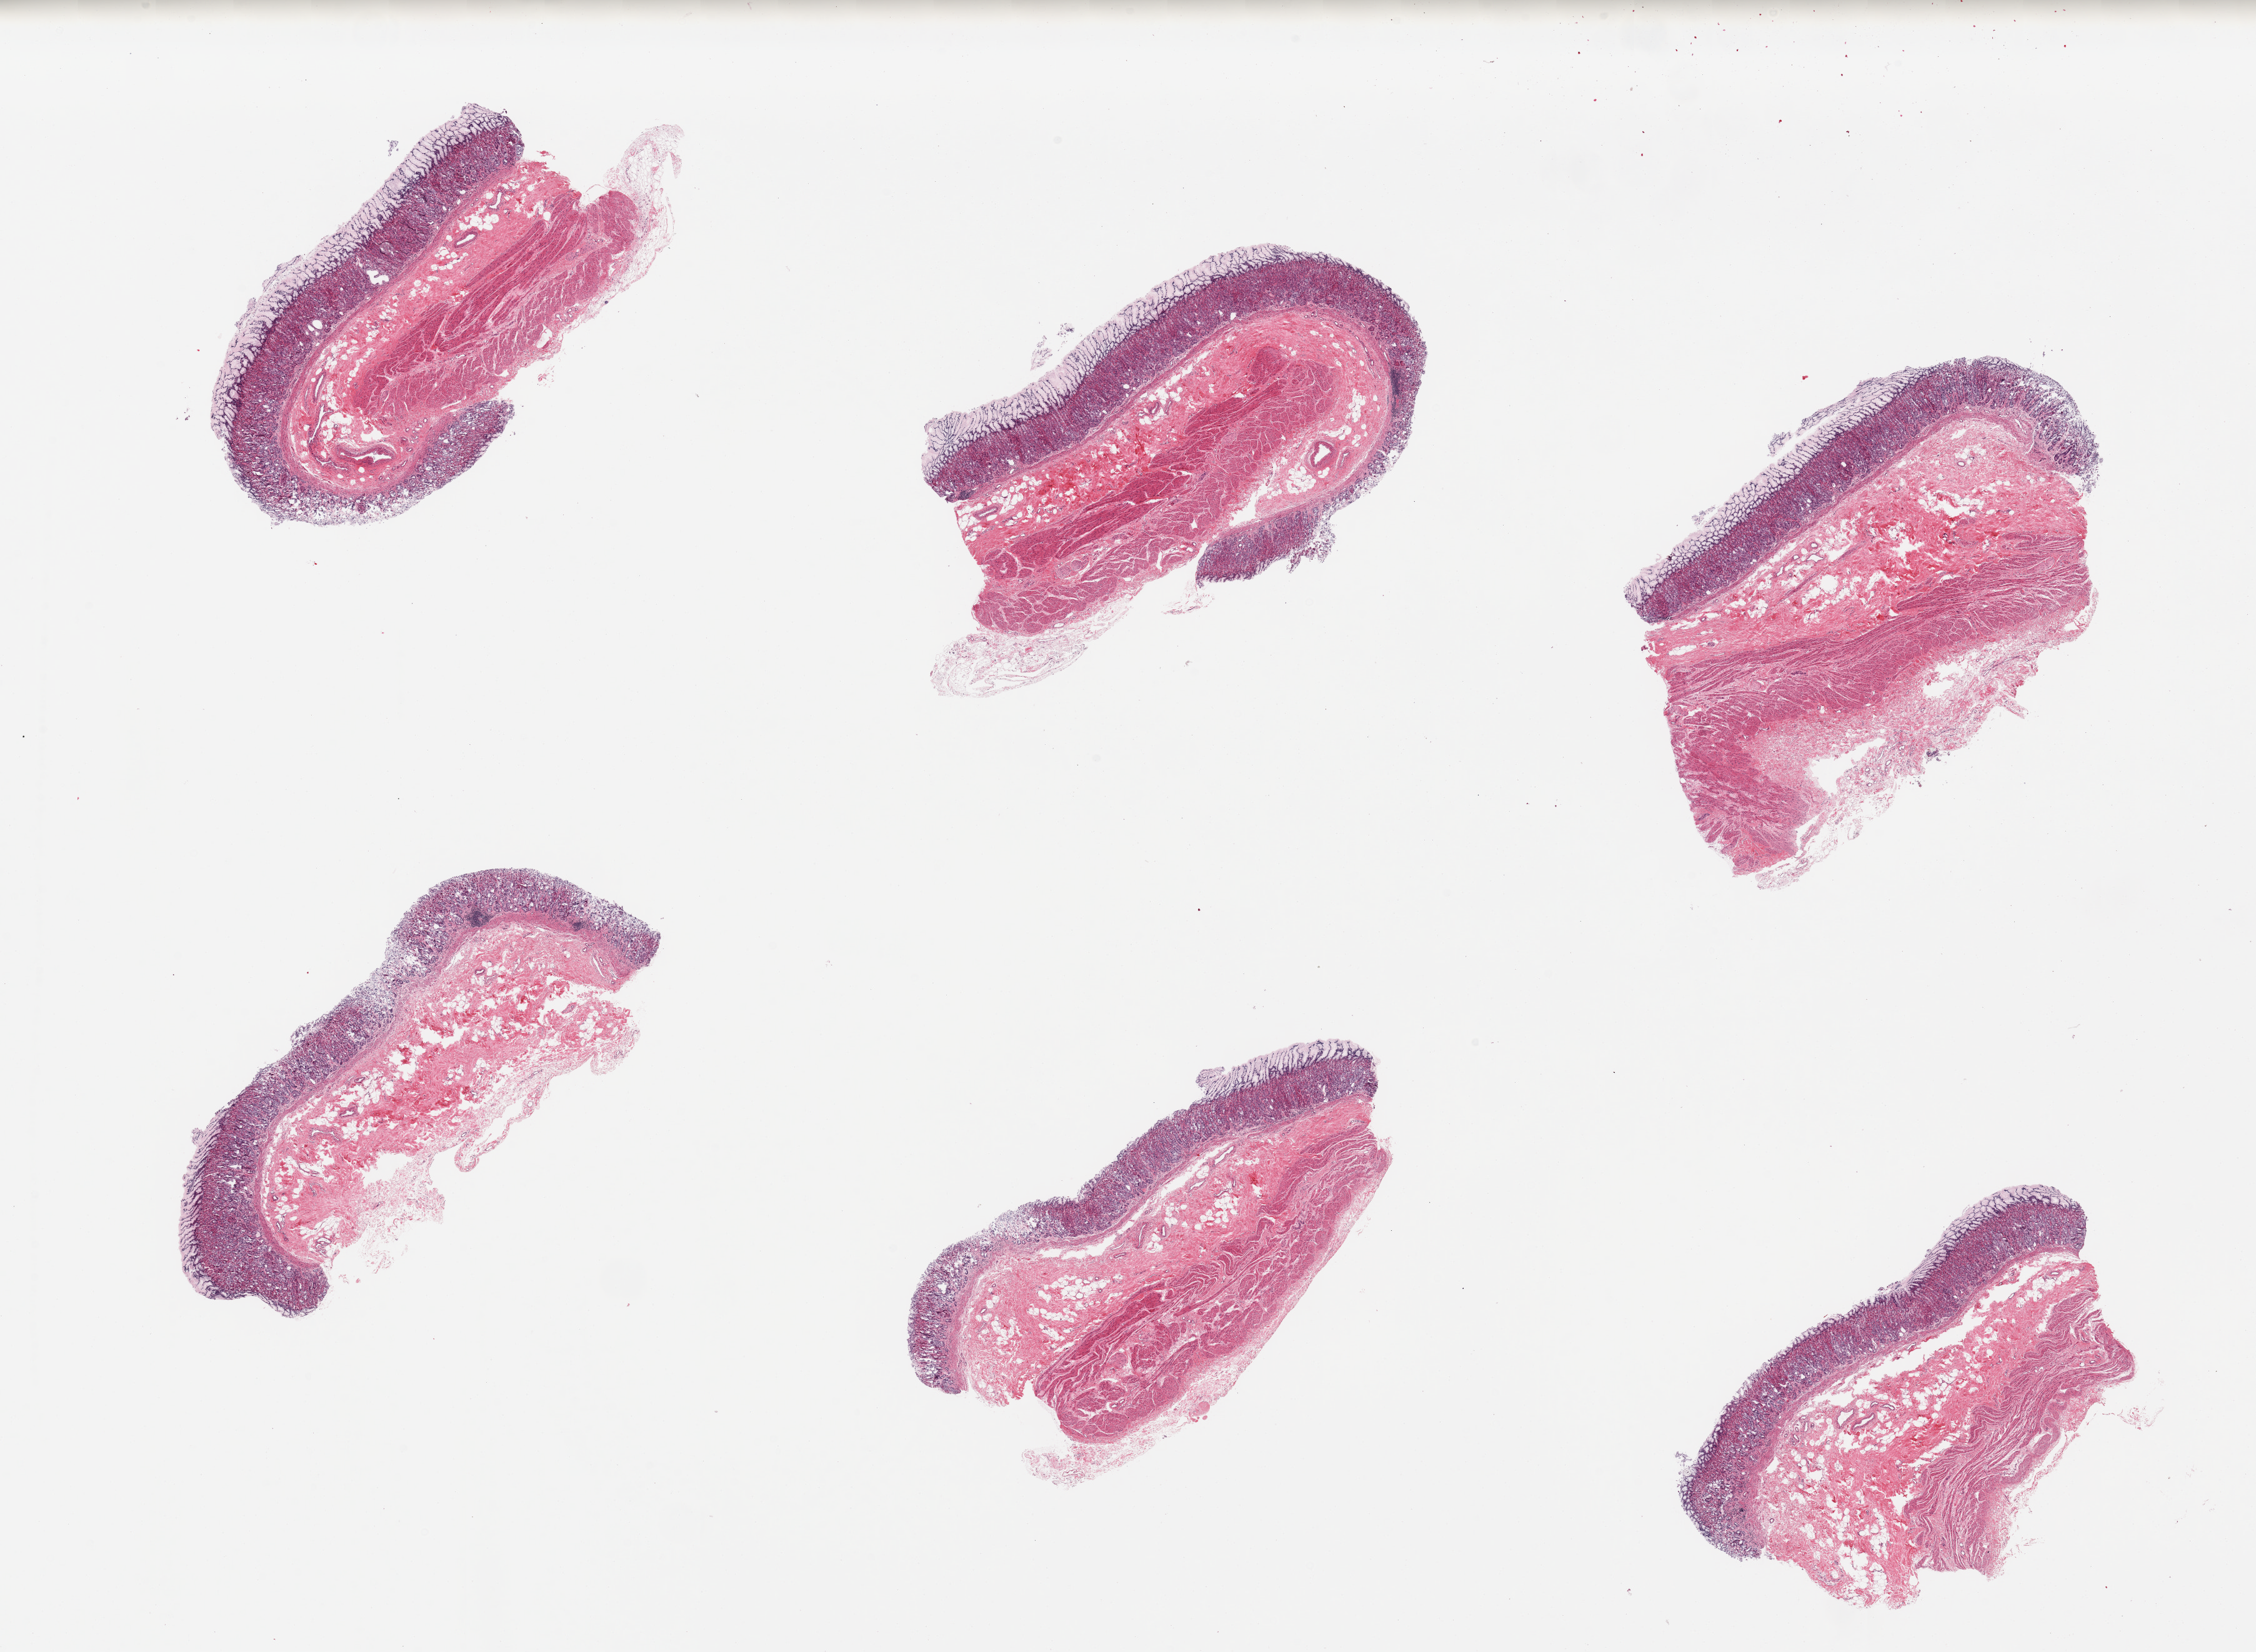
Haematoxylin and eosin whole-slide image, brightfield, whole scanned area (about 28.5 x 20.9 mm) shown as a low-resolution overview; PAXgene-fixed paraffin-embedded (PFPE) section; sampled site (target tissue): stomach; donor tissue sample. Donor: female.
• pathologist's review note for this sample: 6 pieces, mucosa is generally well prserved with a few ares approaching grade 2 with sloughing--mucosa is ~20-30% thickness